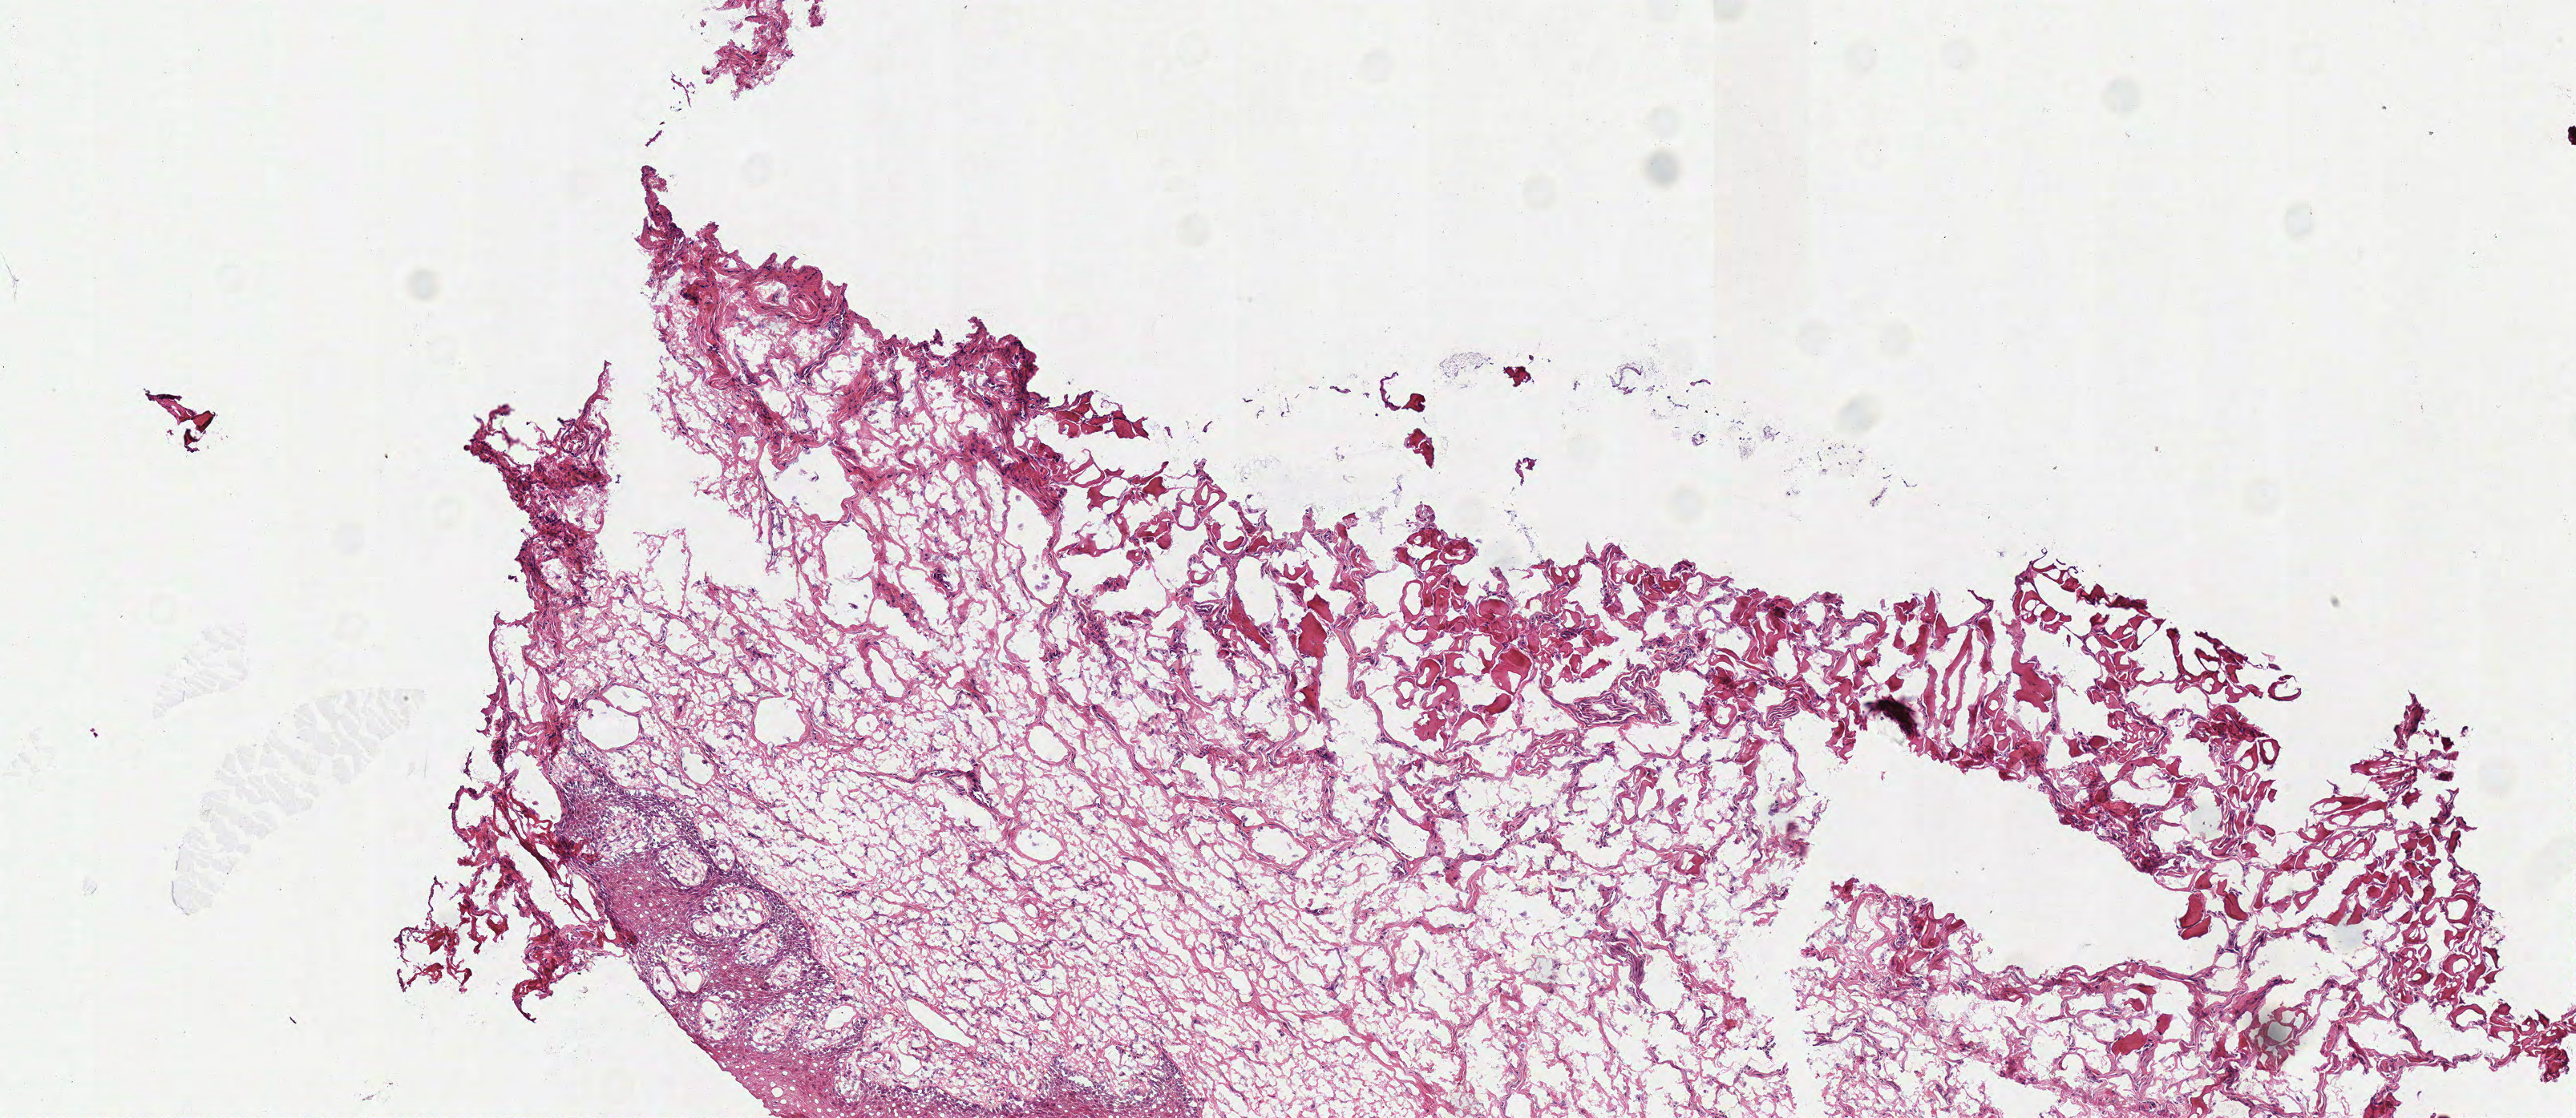
Hematoxylin and eosin (H&E) stained whole-slide image, low-resolution overview of the scanned area, about 6.3 x 2.7 mm, frozen section, solid tissue normal (non-tumour tissue) sample from the head and neck. Patient: male, age at initial diagnosis 61 years.
This section: solid tissue normal (non-tumour) sample from the same patient. Patient diagnosis: Squamous cell carcinoma, NOS (tongue, NOS).